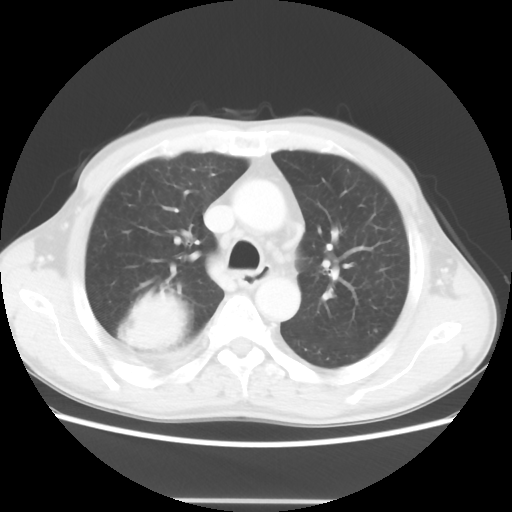
Chest CT, one axial slice; lung window (W 1500 / L -600 HU); 5 mm slice thickness; 512 × 512 image matrix, field of view 361 × 361 mm. Male patient, age 66 years. Case-level facts recorded for this patient, not image findings: clinical TNM (as recorded): T4 N1 M1.
Outlined on this slice (rectangle marked by the reading radiologist):
- lung tumour (recorded histology: small cell carcinoma): box from (x=118, y=283) to (x=188, y=358) px